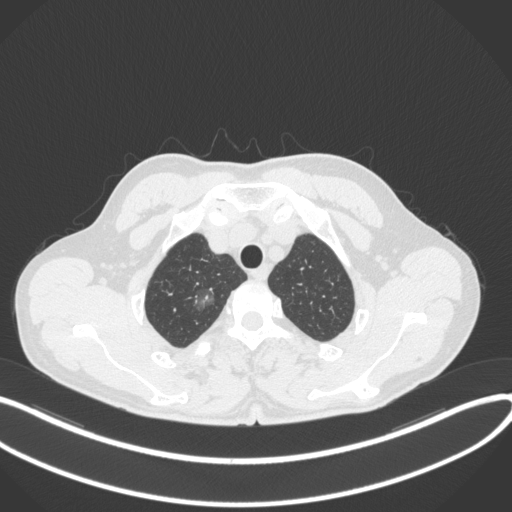
Chest CT, one axial slice; slice 330 of 407 in the series (ordered by position); reconstruction kernel B31f; 120 kVp; lung window (W 1500 / L -600 HU); 512 × 512 image matrix. Patient: male, 58 years. From the clinical record (not read from this slice): clinical TNM (as recorded): T1c N0 M0.
Outlined on this slice (rectangle marked by the reading radiologist):
- lung tumour (recorded histology: adenocarcinoma): bounding box (x1, y1, x2, y2) in pixels: (192, 282, 217, 312)